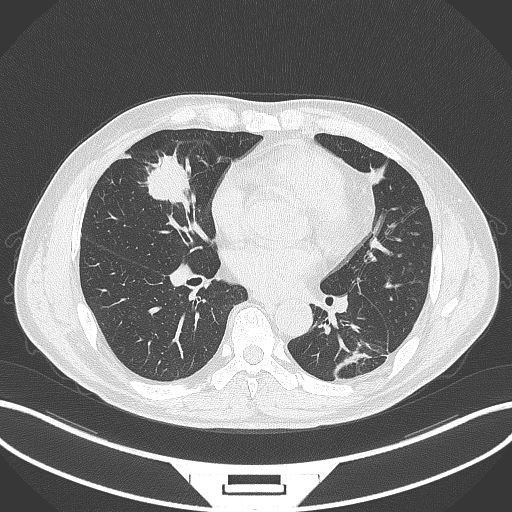
Chest CT, one axial slice; slice 133 of 399 in the series (ordered by position); 120 kVp; lung window (W 1500 / L -600 HU); 1 mm slice thickness; 512 × 512 image matrix, field of view 400 × 400 mm. Patient: male, 59 years. Case-level facts recorded for this patient, not image findings: clinical TNM (as recorded): T2a N1 M0.
Annotated regions visible in this slice (bounding box drawn by a radiologist):
- lung tumour (recorded histology: adenocarcinoma): bounding box [x1, y1, x2, y2] px = [144, 152, 194, 206]